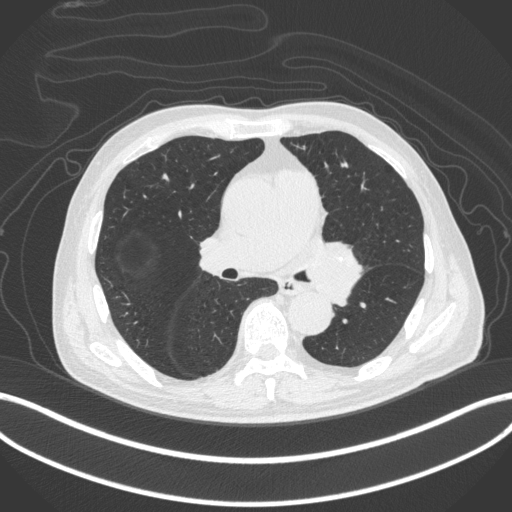
Chest CT, one axial slice. Position 243 of 420 along the scan axis. Reconstruction kernel B31f. Lung window (W 1500 / L -600 HU). 1 mm slice thickness. 512 × 512 image matrix. Male patient, age 77 years. From the clinical record (not read from this slice): clinical TNM (as recorded): T3 N1 M0.
Annotated regions visible in this slice (bounding box drawn by a radiologist):
- lung tumour (recorded histology: adenocarcinoma): bounding box <305,235,365,302> (left, top, right, bottom; pixels)